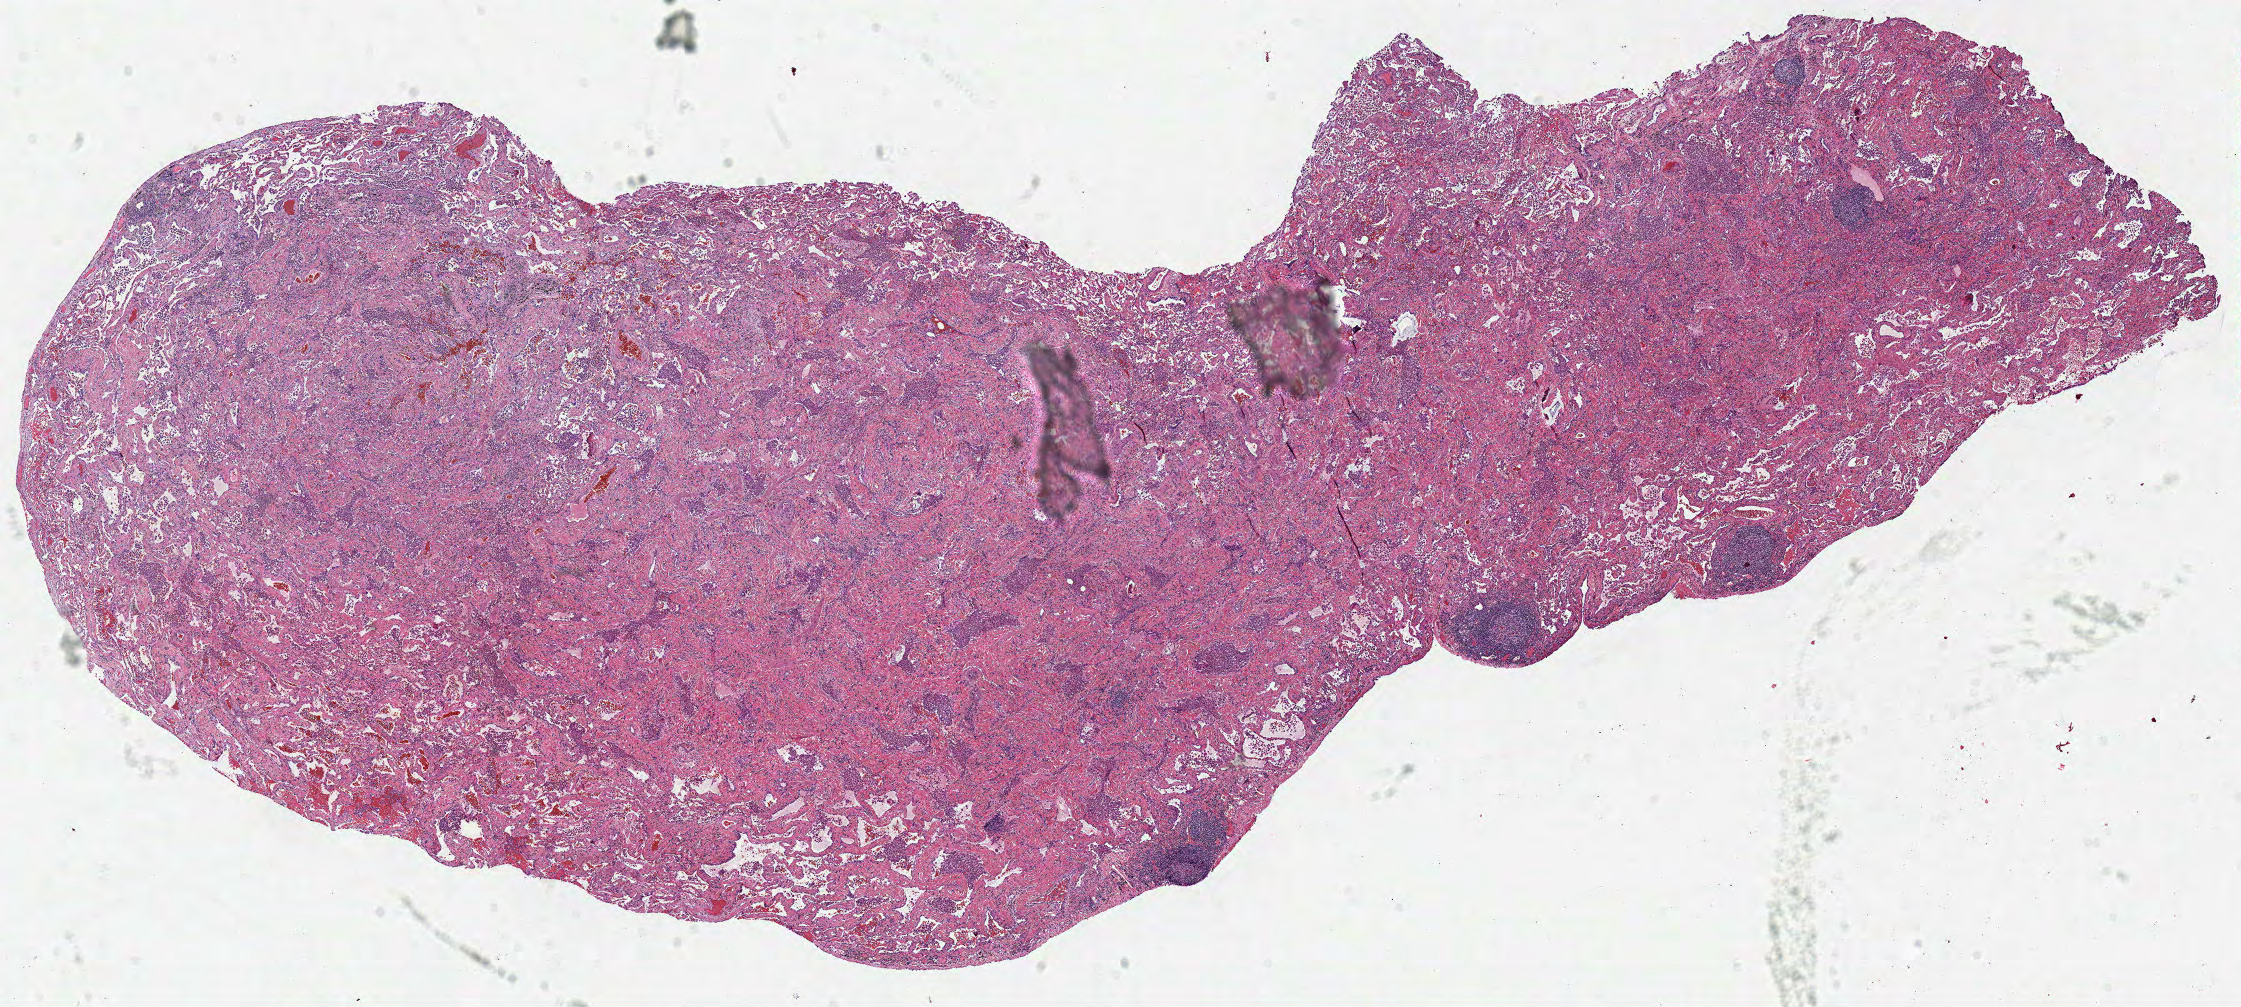
Hematoxylin and eosin (H&E) stained whole-slide image, a low-resolution overview of the entire scanned area, about 17.6 x 7.9 mm (slide scanned at 40x), frozen section from the top of the tissue portion, lung, solid tissue normal (non-tumour tissue) sample. Female patient; age at initial diagnosis 59 years.
This section: solid tissue normal (non-tumour) sample from the same patient. Patient diagnosis: Squamous cell carcinoma, NOS (upper lobe, lung).